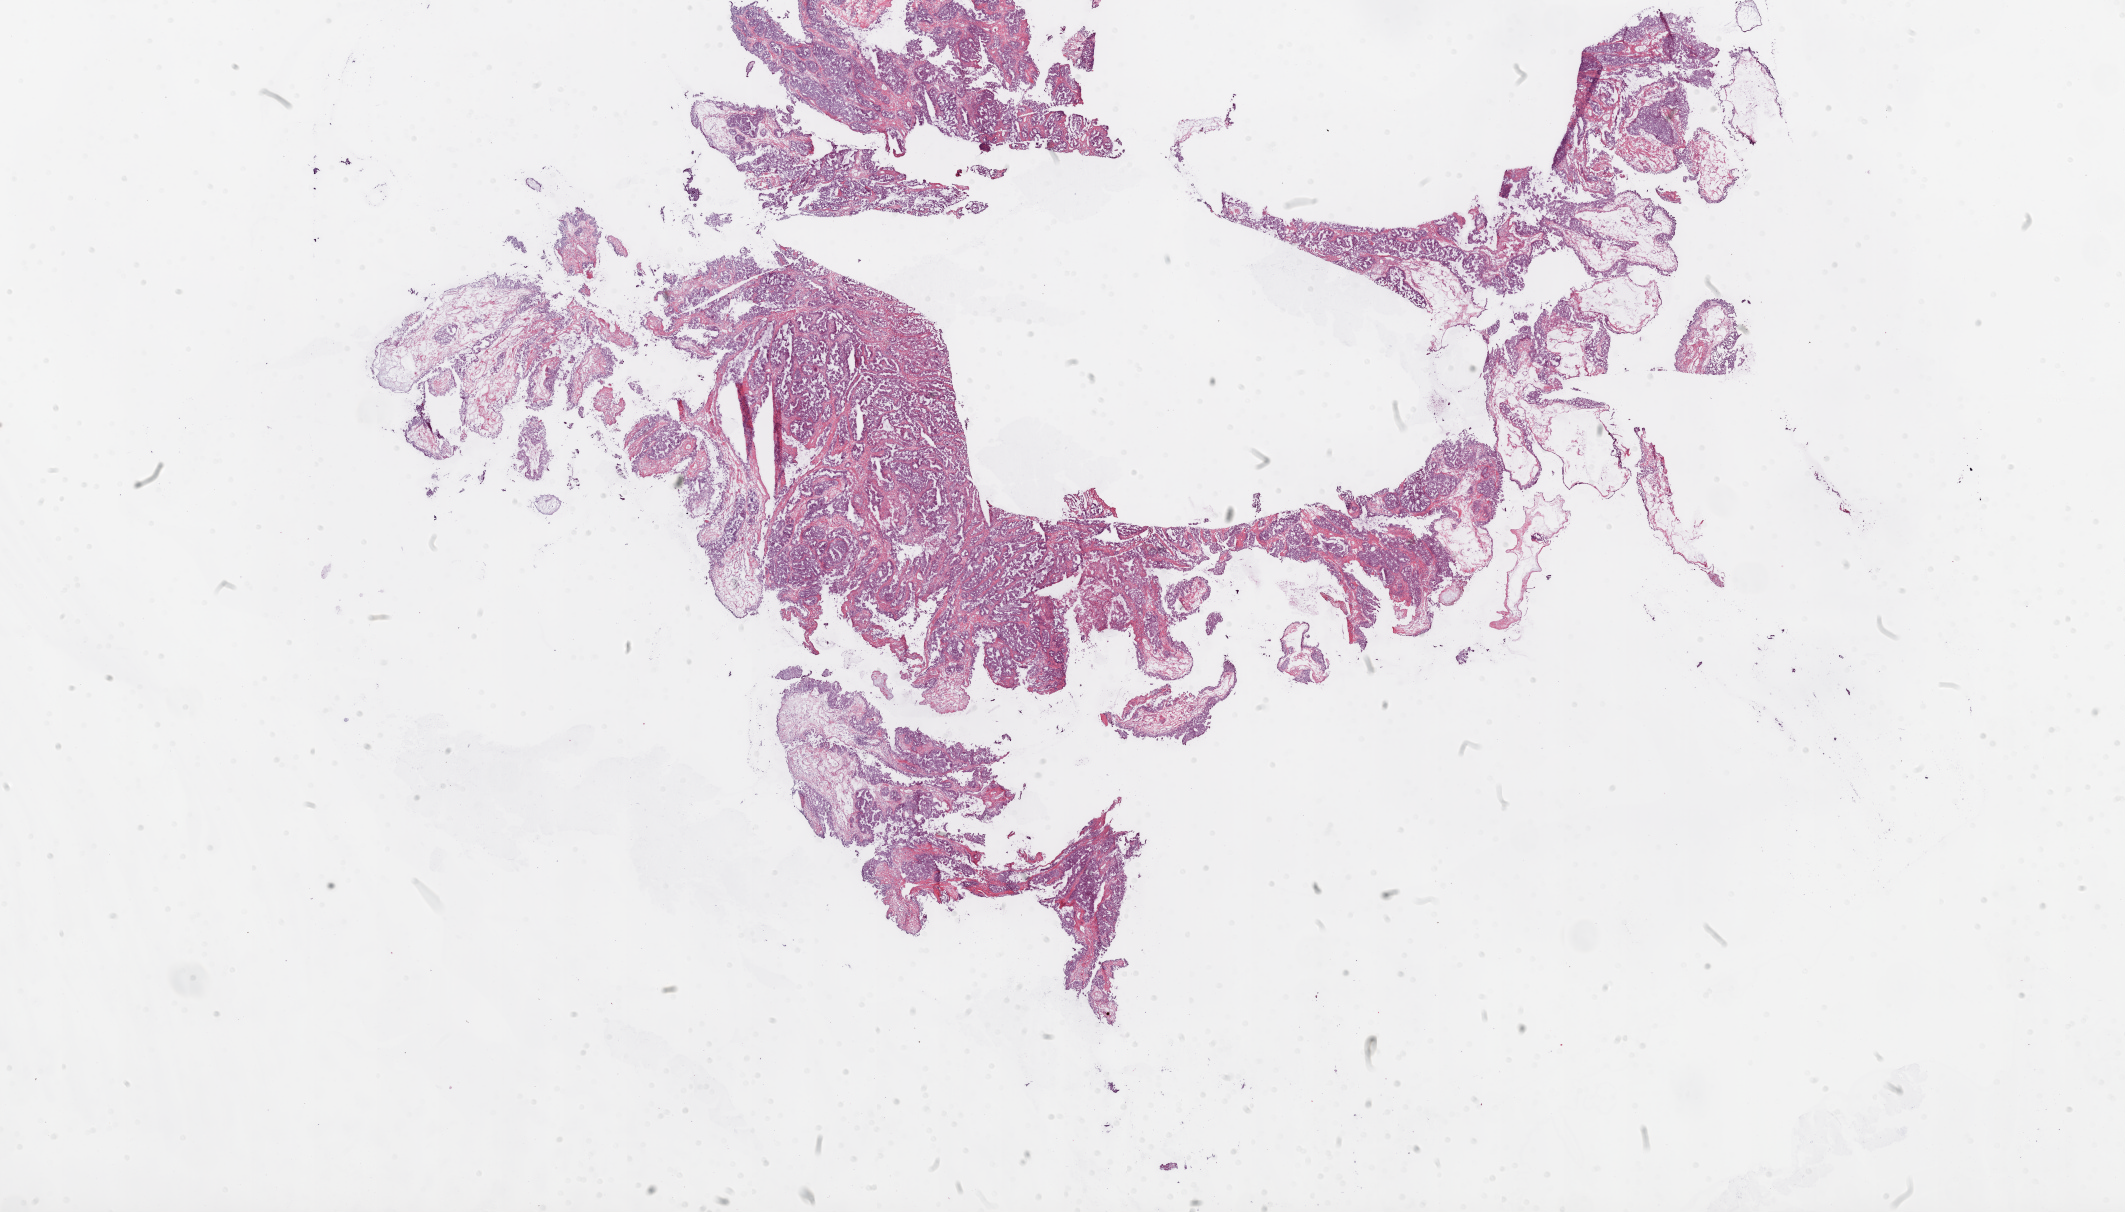
Hematoxylin and eosin (H&E) stained whole-slide image — low-resolution overview of the scanned area, about 34.1 x 19.5 mm (slide scanned at 20x). Frozen section. Sample: primary tumour, ovary. Female, age 69 years at initial diagnosis. Histologic grade: G3 (poorly differentiated). Pathologist review of this section (percent, as recorded): tumour cells 90%, tumour nuclei 90%, normal cells 0%, stromal cells 10%, necrosis 0%.
Histologic diagnosis: Serous cystadenocarcinoma, NOS. FIGO stage: IC. Laterality: left.